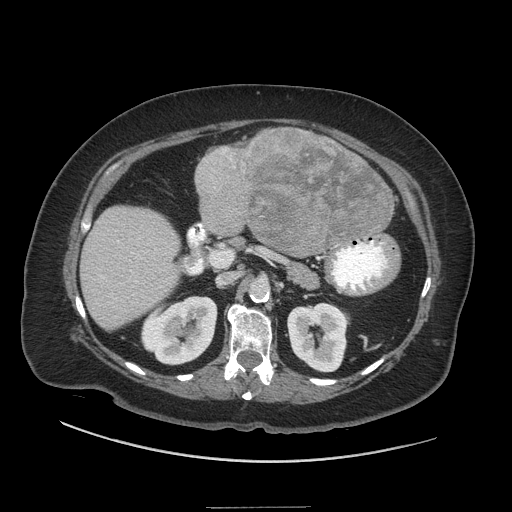
Contrast-enhanced abdominal CT (liver protocol), one axial slice; slice 14 of 81 in the series (ordered by position); reconstruction kernel STANDARD; 140 kVp; soft-tissue window (W 400 / L 40 HU); 512 × 512 image matrix, field of view 440 × 440 mm. Case-level facts recorded for this patient, not image findings: diagnosis: hepatocellular carcinoma (patient treated with transarterial chemoembolisation; whether this scan precedes or follows treatment is not stated here); TNM stage (as recorded): Stage-II; Child-Pugh class: A; tumour nodularity: multinodular; tumour size: 1.7 cm.
Structures marked on this image (semi-automatic segmentation, software-assisted and operator-edited):
- liver parenchyma outside the tumour (the mass and vessels are separate outlines, so this box may not span the whole liver): bounding box (x1, y1, x2, y2) in pixels: (80, 128, 392, 330)
- mass: (195, 127, 398, 255)
- liver vessels: (100, 241, 163, 288)